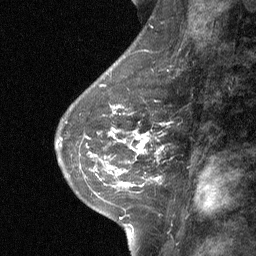
Breast MRI (dynamic contrast-enhanced), one sagittal slice; position 27 of 64 along the scan axis; dynamic contrast-enhanced study with each time point stored as its own series, time point 2 of 3 at this slice position (early post-contrast, ordered by acquisition time); 1.5 T; TE 4.8 ms, TR 27 ms; 2 mm slice thickness; 256 × 256 image matrix, field of view 180 × 180 mm. Patient: female, 42 years. From the clinical record (not read from this slice): setting: breast cancer imaged before/during neoadjuvant chemotherapy; receptor status: triple-negative.
Annotated regions visible in this slice (semi-automatically segmented with operator editing):
- analysis volume of interest (the breast-tissue region the enhancement analysis was run in; not a lesion): bounding box (x1, y1, x2, y2) in pixels: (99, 117, 174, 187)
- tumour enhancement mask (voxels above the 90 % enhancement threshold inside the analysis volume of interest): (113, 132, 163, 180)